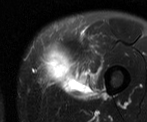
MRI of an extremity soft-tissue mass, one axial slice; slice 13 of 52 in the series (ordered by position); T2-weighted fat-saturated; MR volume resampled by the dataset authors to the PET/CT grid (not the native acquisition matrix); 3.27 mm slice thickness; 147 × 122 image matrix, field of view 144 × 119 mm. Male patient. Case-level facts recorded for this patient, not image findings: histological type: pleiomorphic liposarcoma; grade: high; site of the primary tumour: left thigh.
Outlined on this slice (expert contour drawn on MRI and transferred to this co-registered scan by the dataset authors):
- gross tumour volume including surrounding oedema: bounding box (x1, y1, x2, y2) in pixels: (37, 41, 101, 99)
- gross tumour volume (mass): (37, 39, 76, 88)